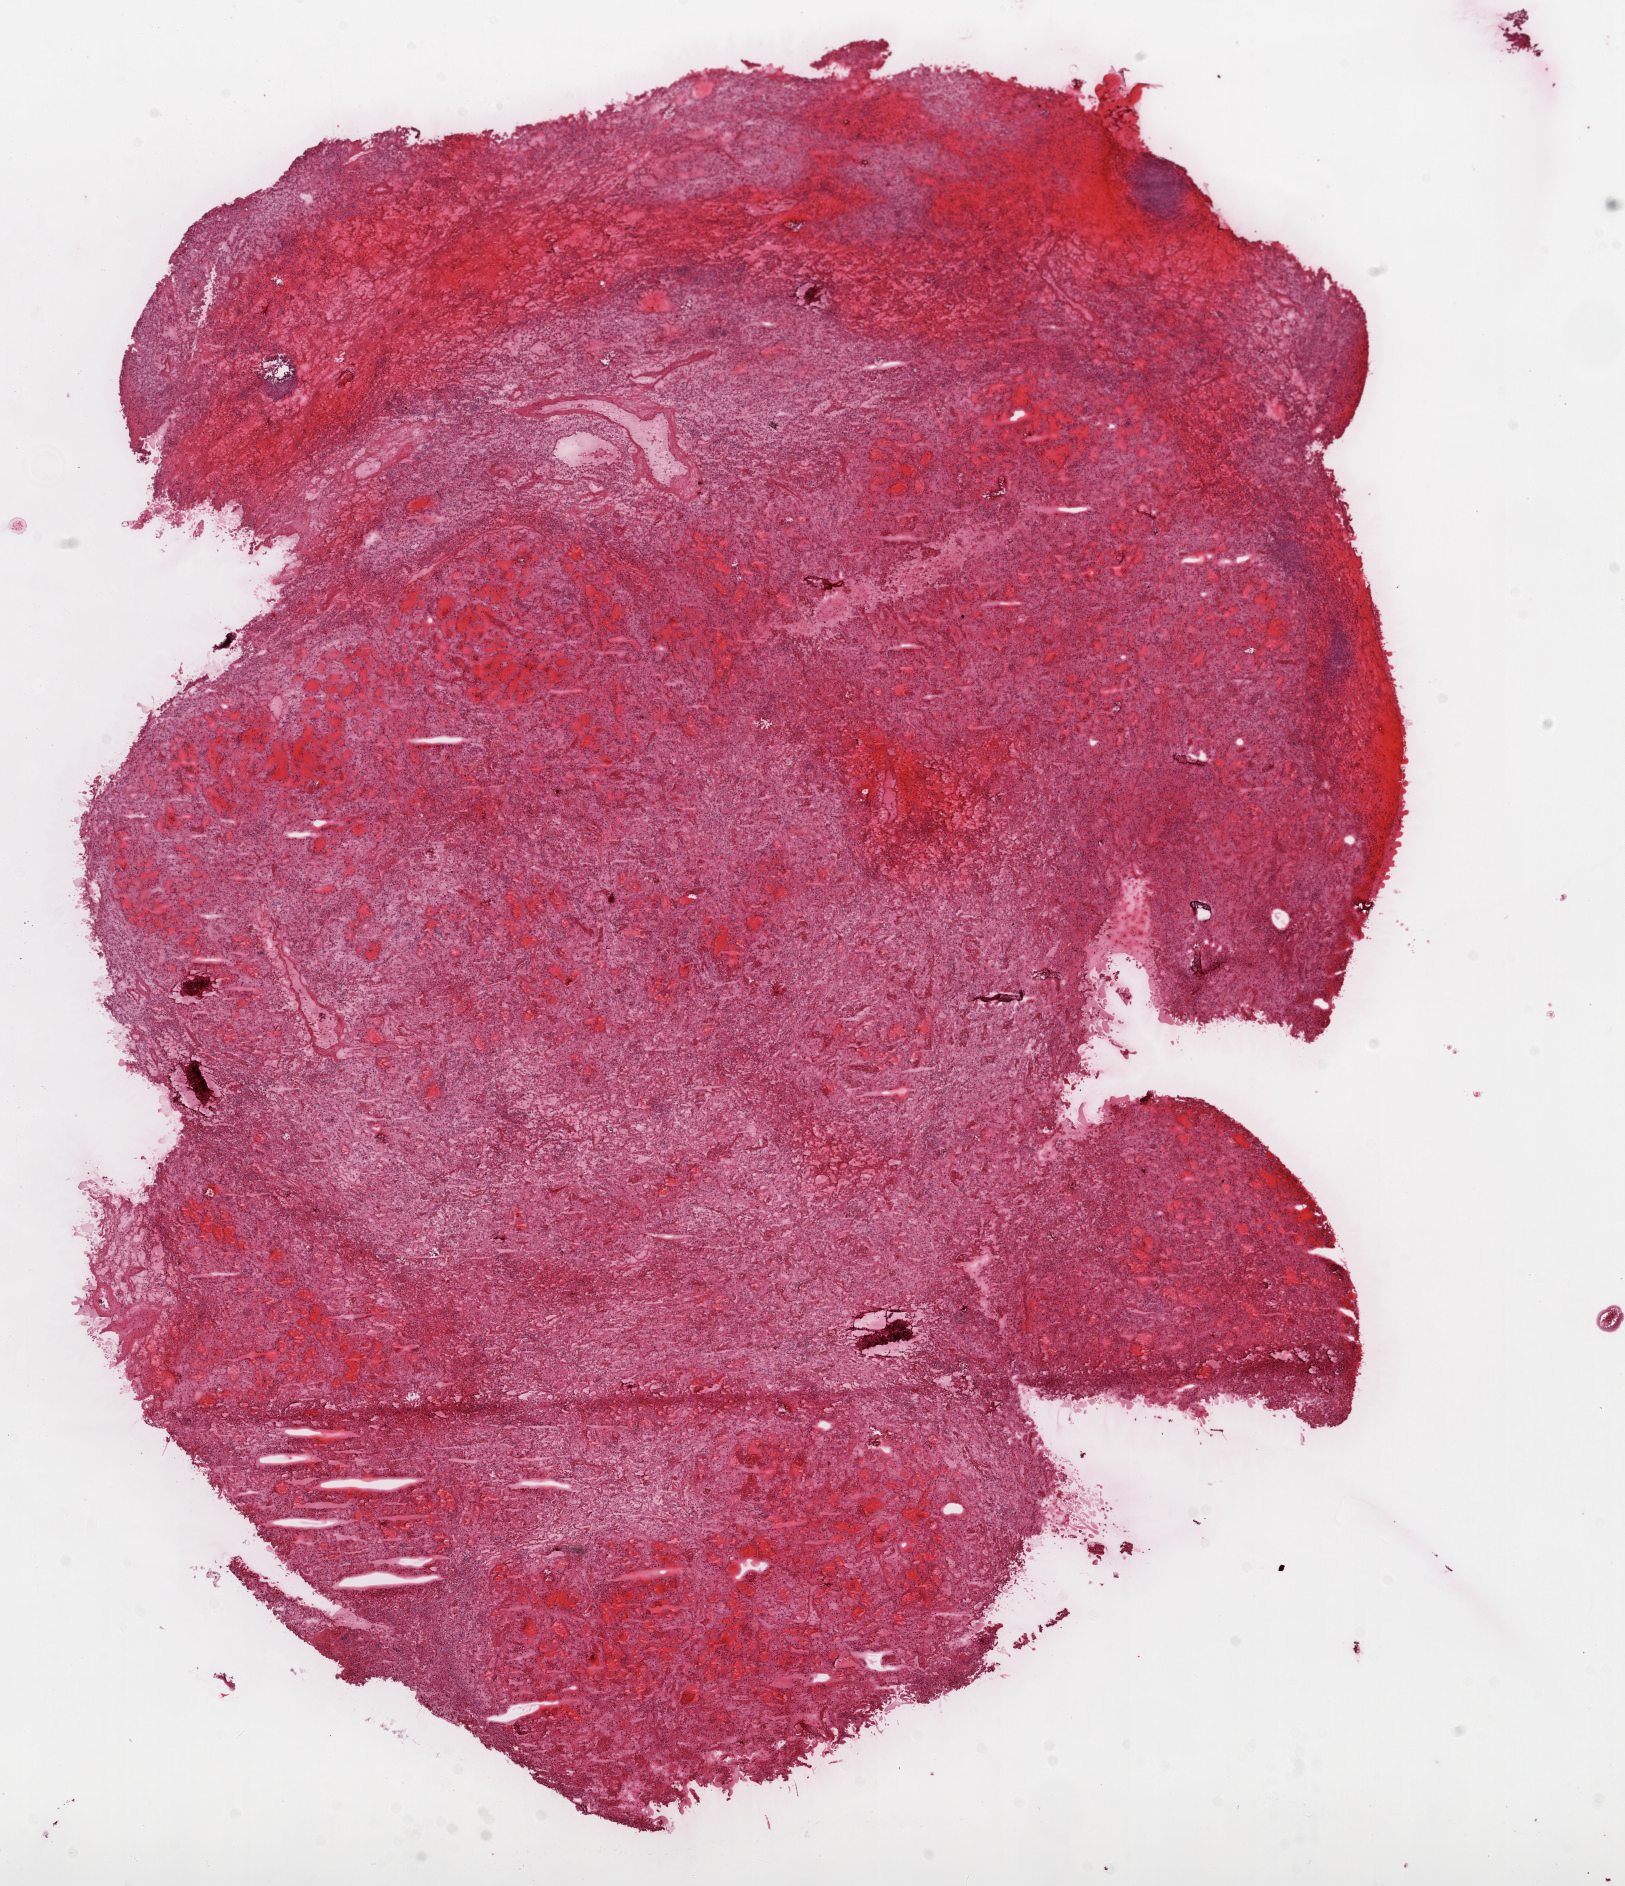
Whole-slide histology image, H&E-stained — a low-resolution overview of the entire scanned area, about 13.0 x 15.1 mm, frozen section, kidney, primary tumour sample. Male patient; age at initial diagnosis 72 years. Slide review estimates, as recorded: tumour cells 95%, tumour nuclei 85%.
Diagnosis: Clear cell adenocarcinoma, NOS.